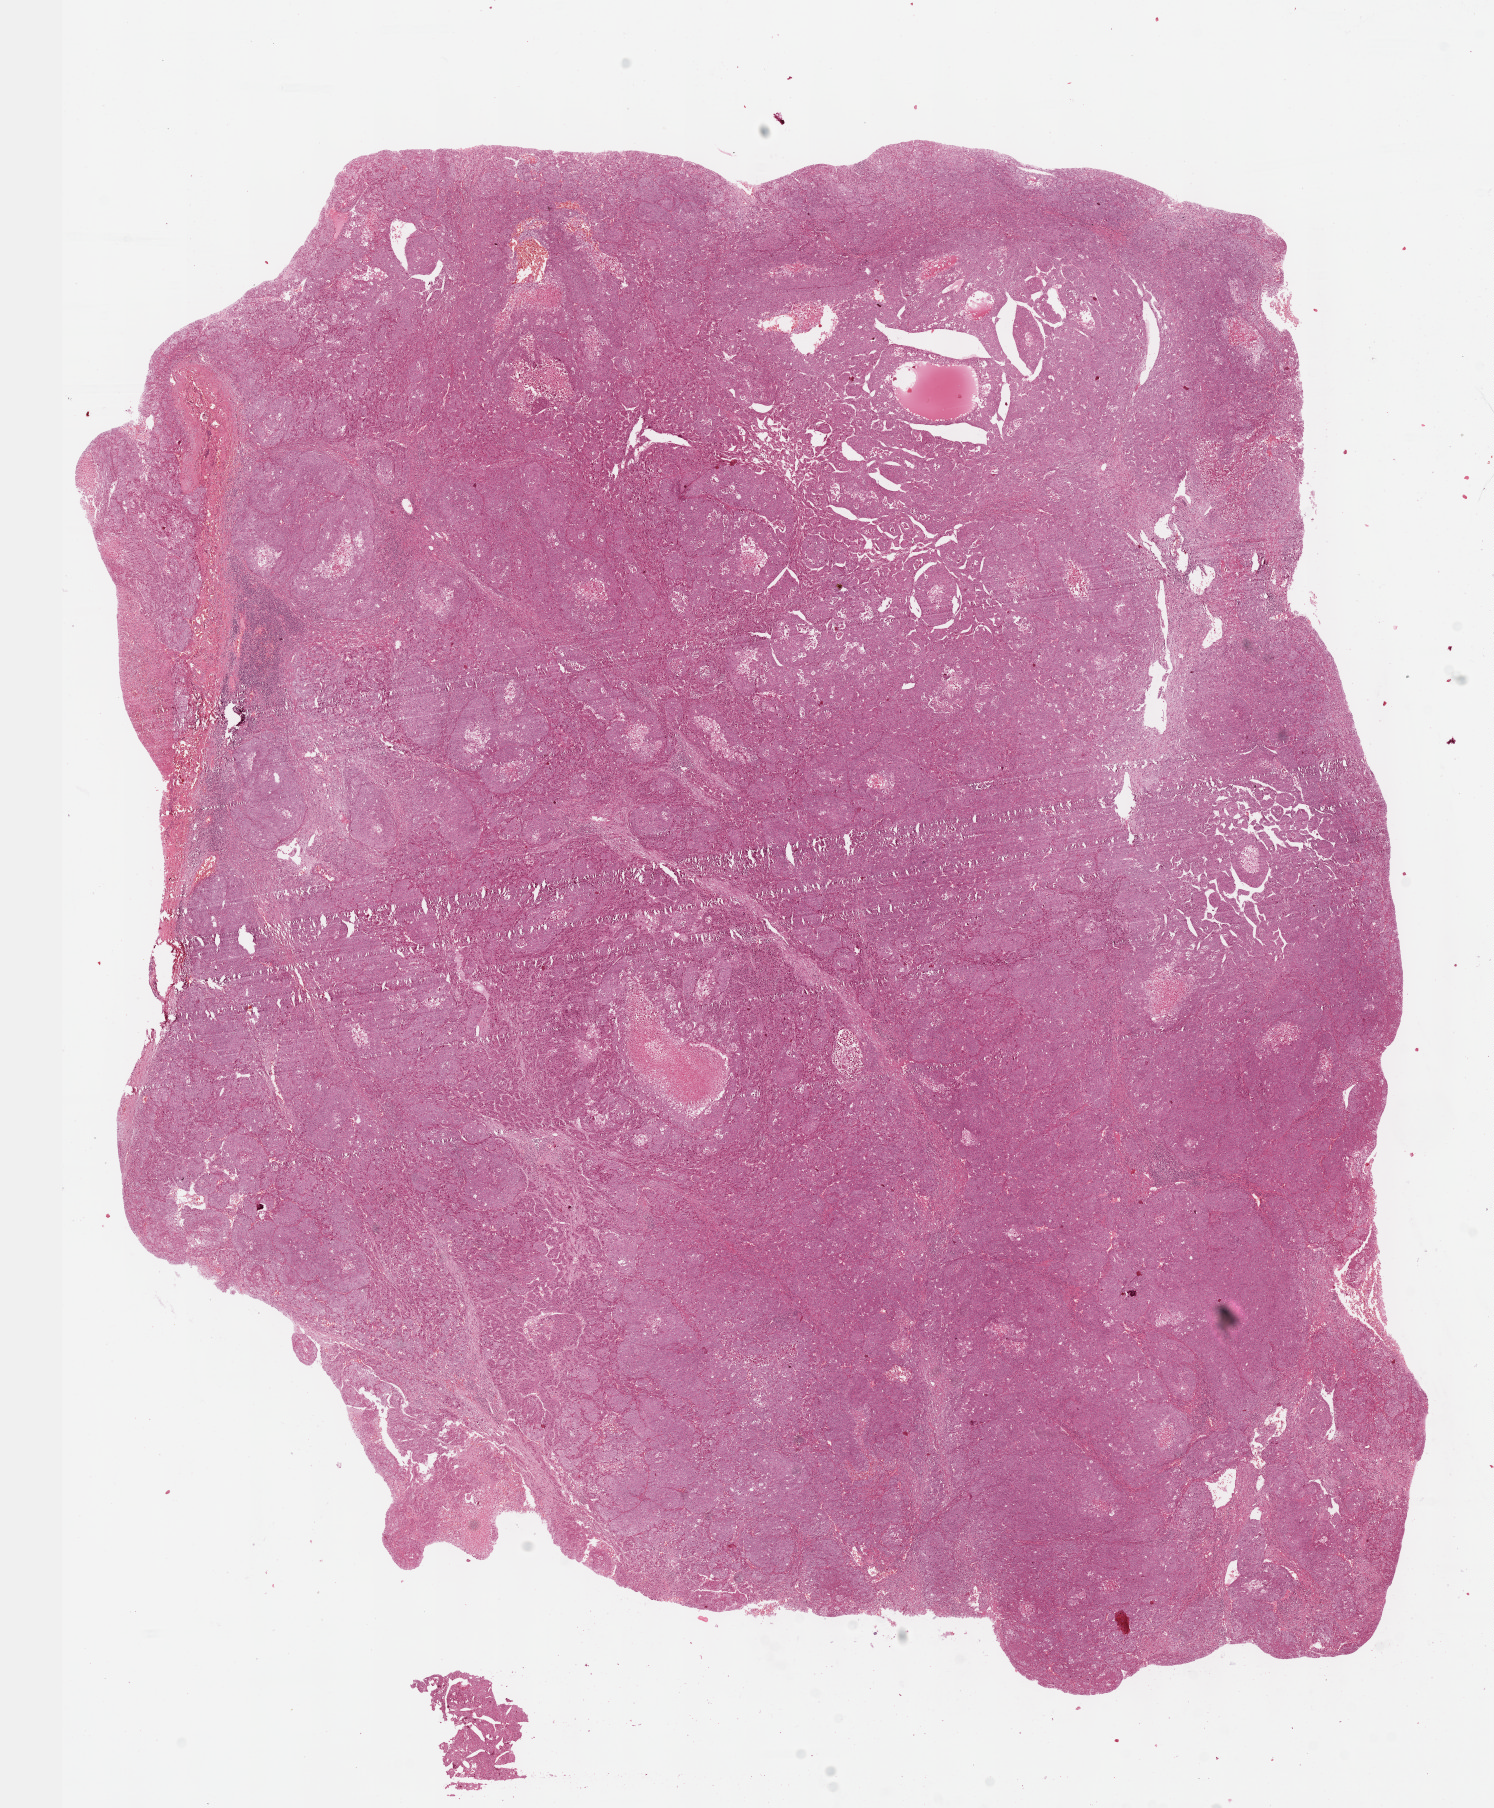
Digitized H&E tissue section (whole slide) — low-resolution overview of the scanned area, about 12.1 x 14.6 mm (acquisition: 40x scan); formalin-fixed paraffin-embedded (FFPE) diagnostic section; liver, primary tumour sample. Patient: male, age at initial diagnosis 57 years. Histologic grade: G2 (moderately differentiated).
- histologic diagnosis: Hepatocellular carcinoma, NOS
- AJCC pathologic stage: IIIA (6th edition)